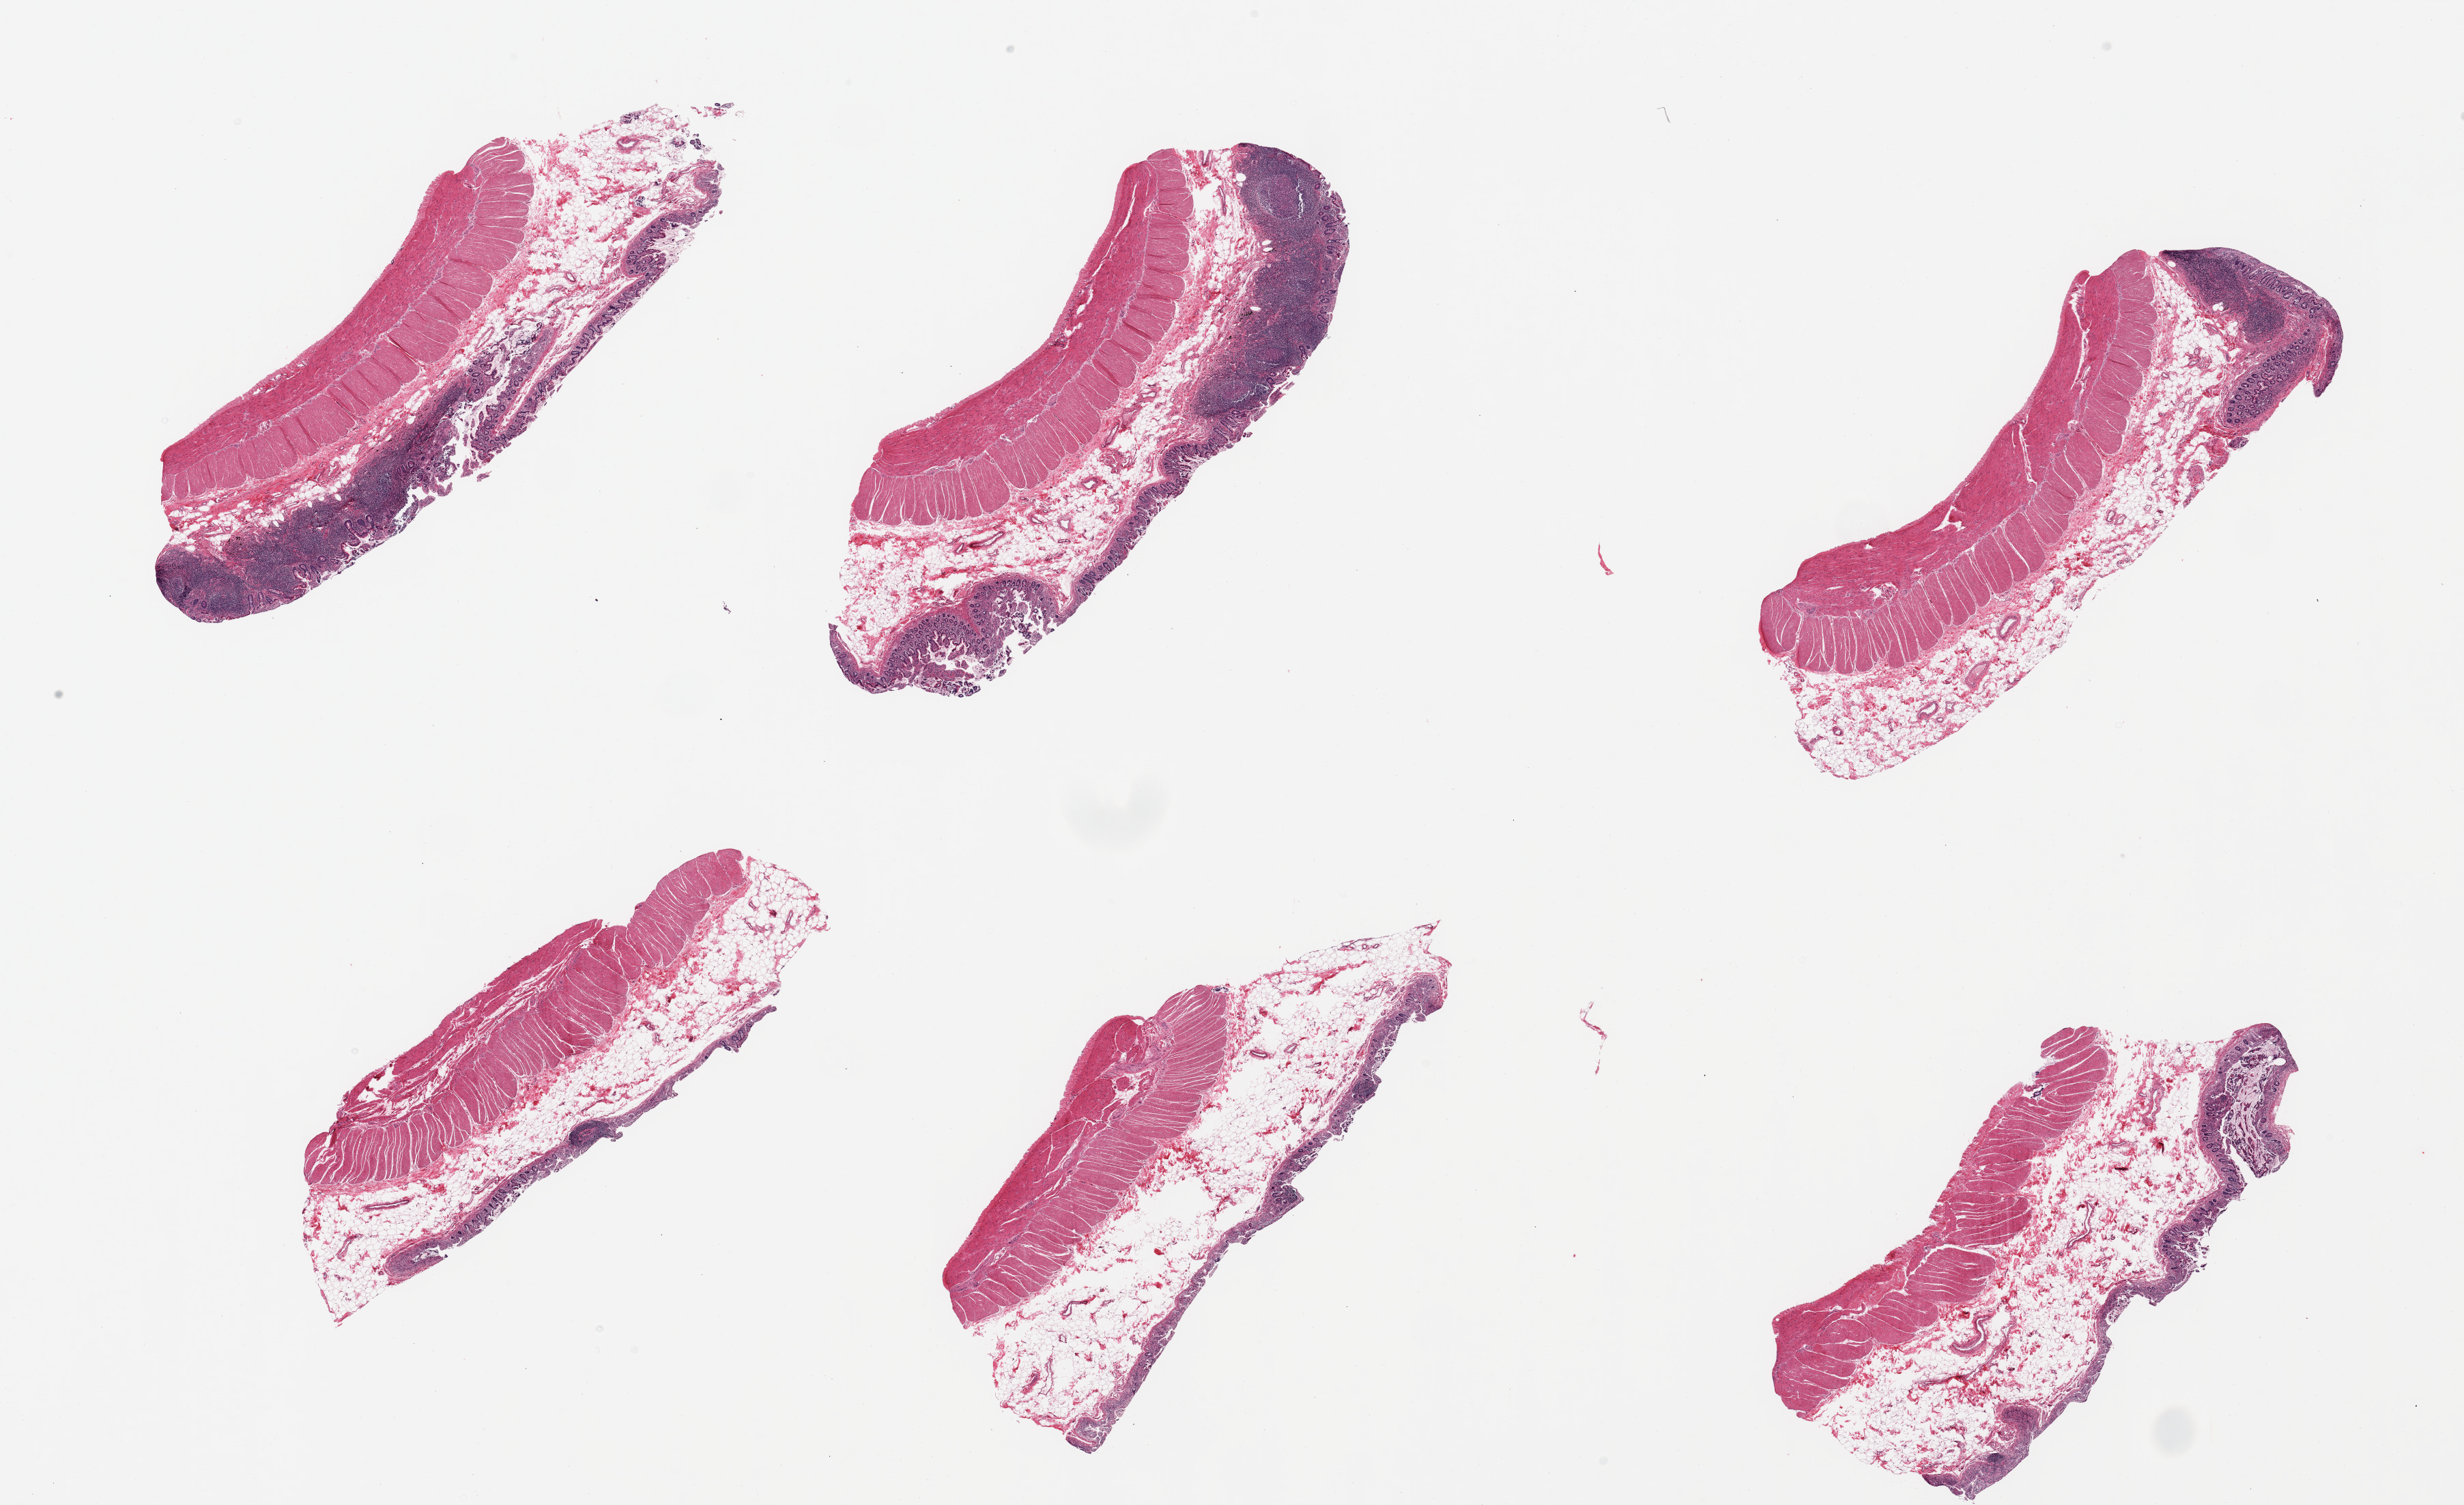
Digitized hematoxylin and eosin (H&E)-stained section — shown as a low-resolution overview of the whole scanned area (about 28.5 x 17.4 mm, from a 20x scan), PAXgene-fixed, paraffin-embedded tissue, target tissue: ileum, tissue donor sample. Donor: male.
- reviewer comment on this tissue sample: 6 pieces, well-fixed target lymphoid aggregates are ~!15% total tissue